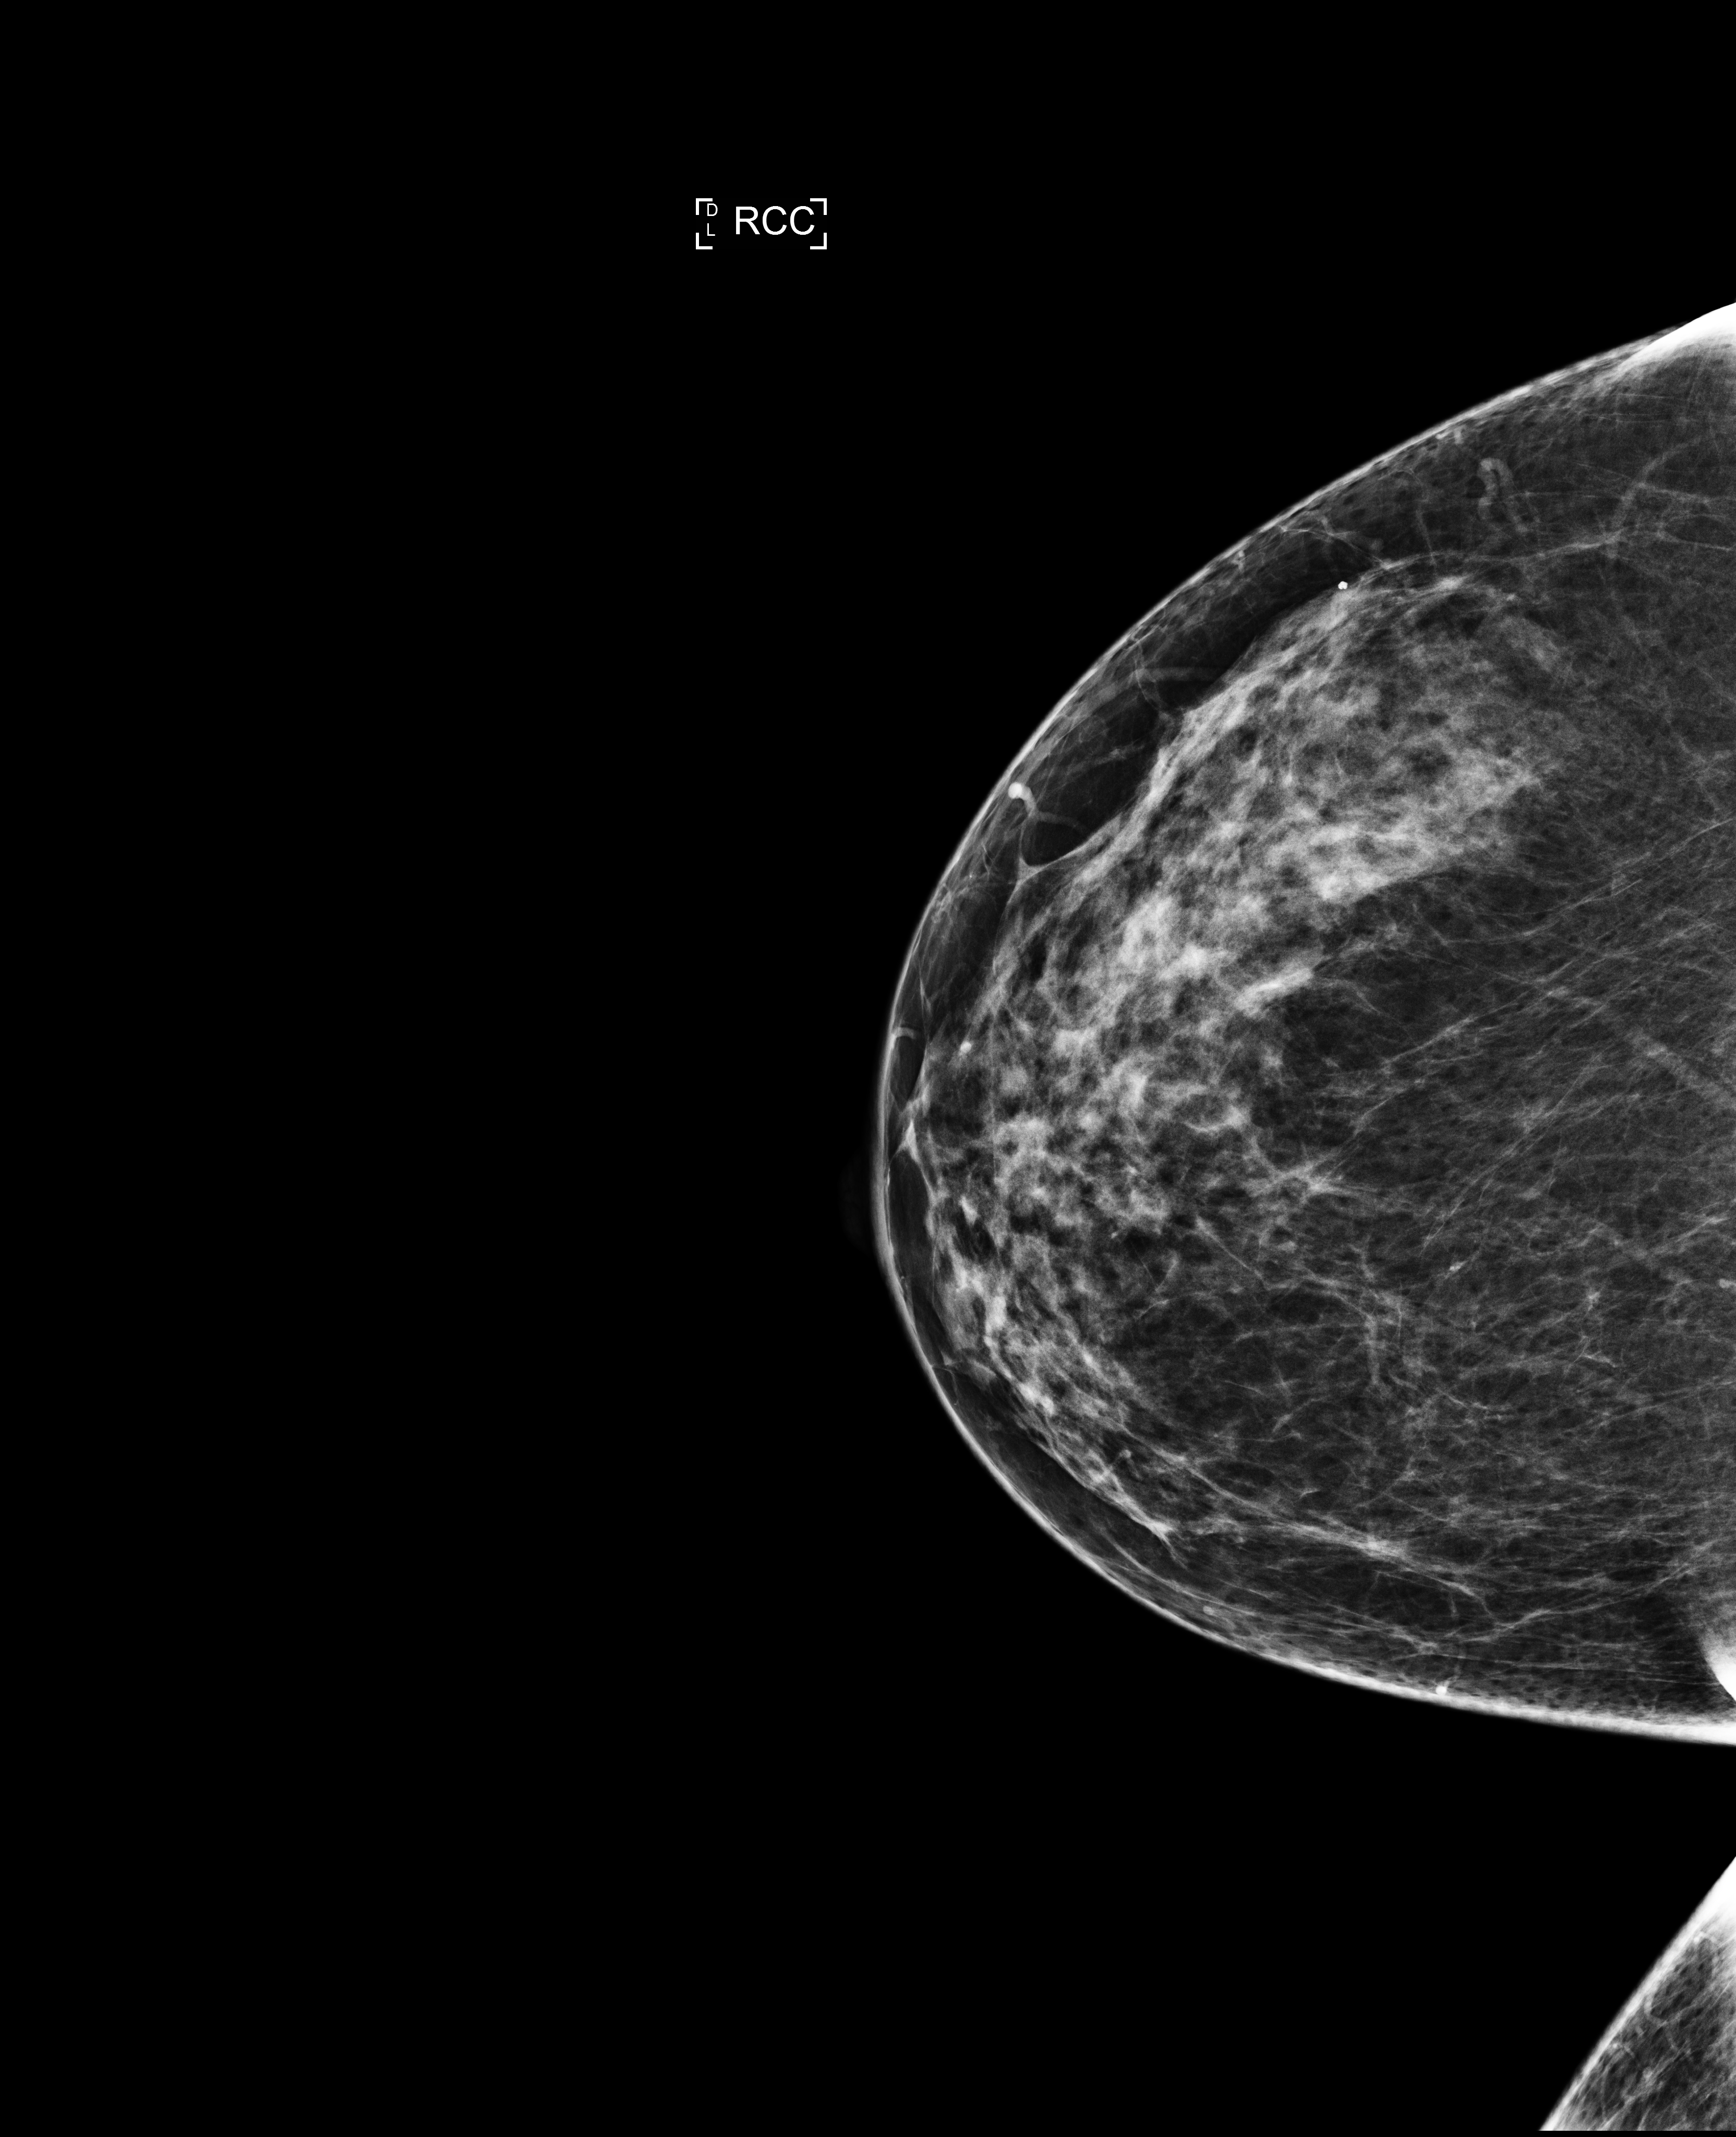
Annual screening mammography examination; compressed breast thickness 63 mm. Patient: female, 47 years.
Image type: full-field digital mammogram. Breast: right. Projection: cranio-caudal projection.